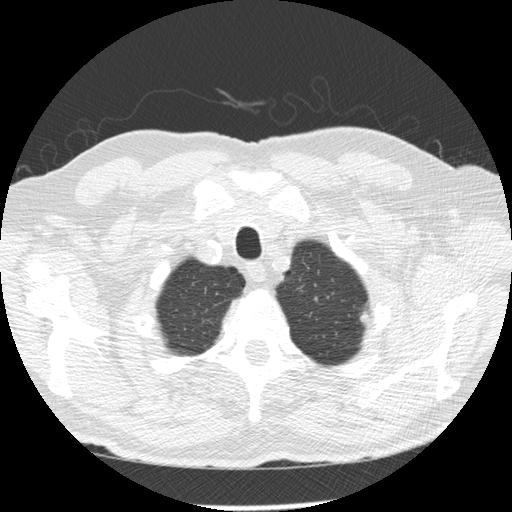
Low-dose screening chest CT, one axial slice. Position 237 of 258 along the scan axis. 120 kVp. Lung window (W 1500 / L -600 HU). 512 × 512 image matrix.
Structures marked on this image (manually delineated by an expert):
- lesion 1 (tumor, upper lobe of left lung): bounding box (x1, y1, x2, y2) in pixels: (360, 311, 369, 325)